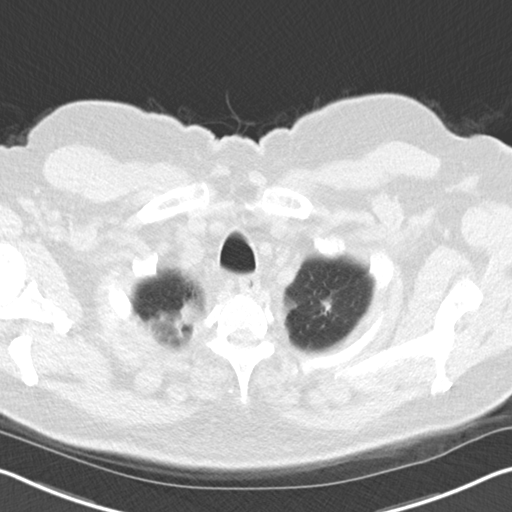
Axial slice from a low-dose chest CT screening exam. Second screening round (one year after baseline). Lung window (W 1500 / L -600 HU). Standard (soft-tissue) reconstruction kernel (B30f). Slice 6 of 68 in the series. 512 × 512 image matrix. Male, age 67 years at enrolment.
- Lesion marked by an expert reader, bounding box [x1, y1, x2, y2] px = [307, 295, 344, 330].
- Screening reader's record for this exam: no non-calcified nodule ≥4 mm recorded.
- Participant outcome: lung cancer diagnosed 507 days after this screen (after the third annual screen) — adenocarcinoma, NOS, left upper lobe, moderately differentiated (G2), stage IIA (AJCC 6th edition), 18 mm at pathology.